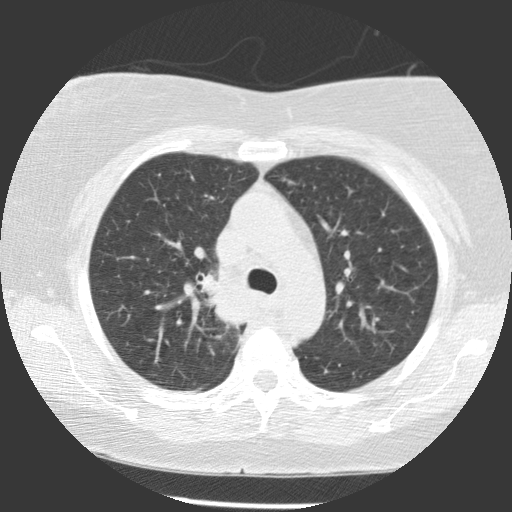
Low-dose screening chest CT, one axial slice. Slice 82 of 116 in the series (ordered by position). Reconstruction kernel STANDARD. Lung window (W 1500 / L -600 HU). 512 × 512 image matrix, field of view 320 × 320 mm.
Outlined on this slice (outlined manually by an expert reader):
- lesion 1 (tumor, upper lobe of right lung): bounding box (x1, y1, x2, y2) in pixels: (201, 273, 245, 330)